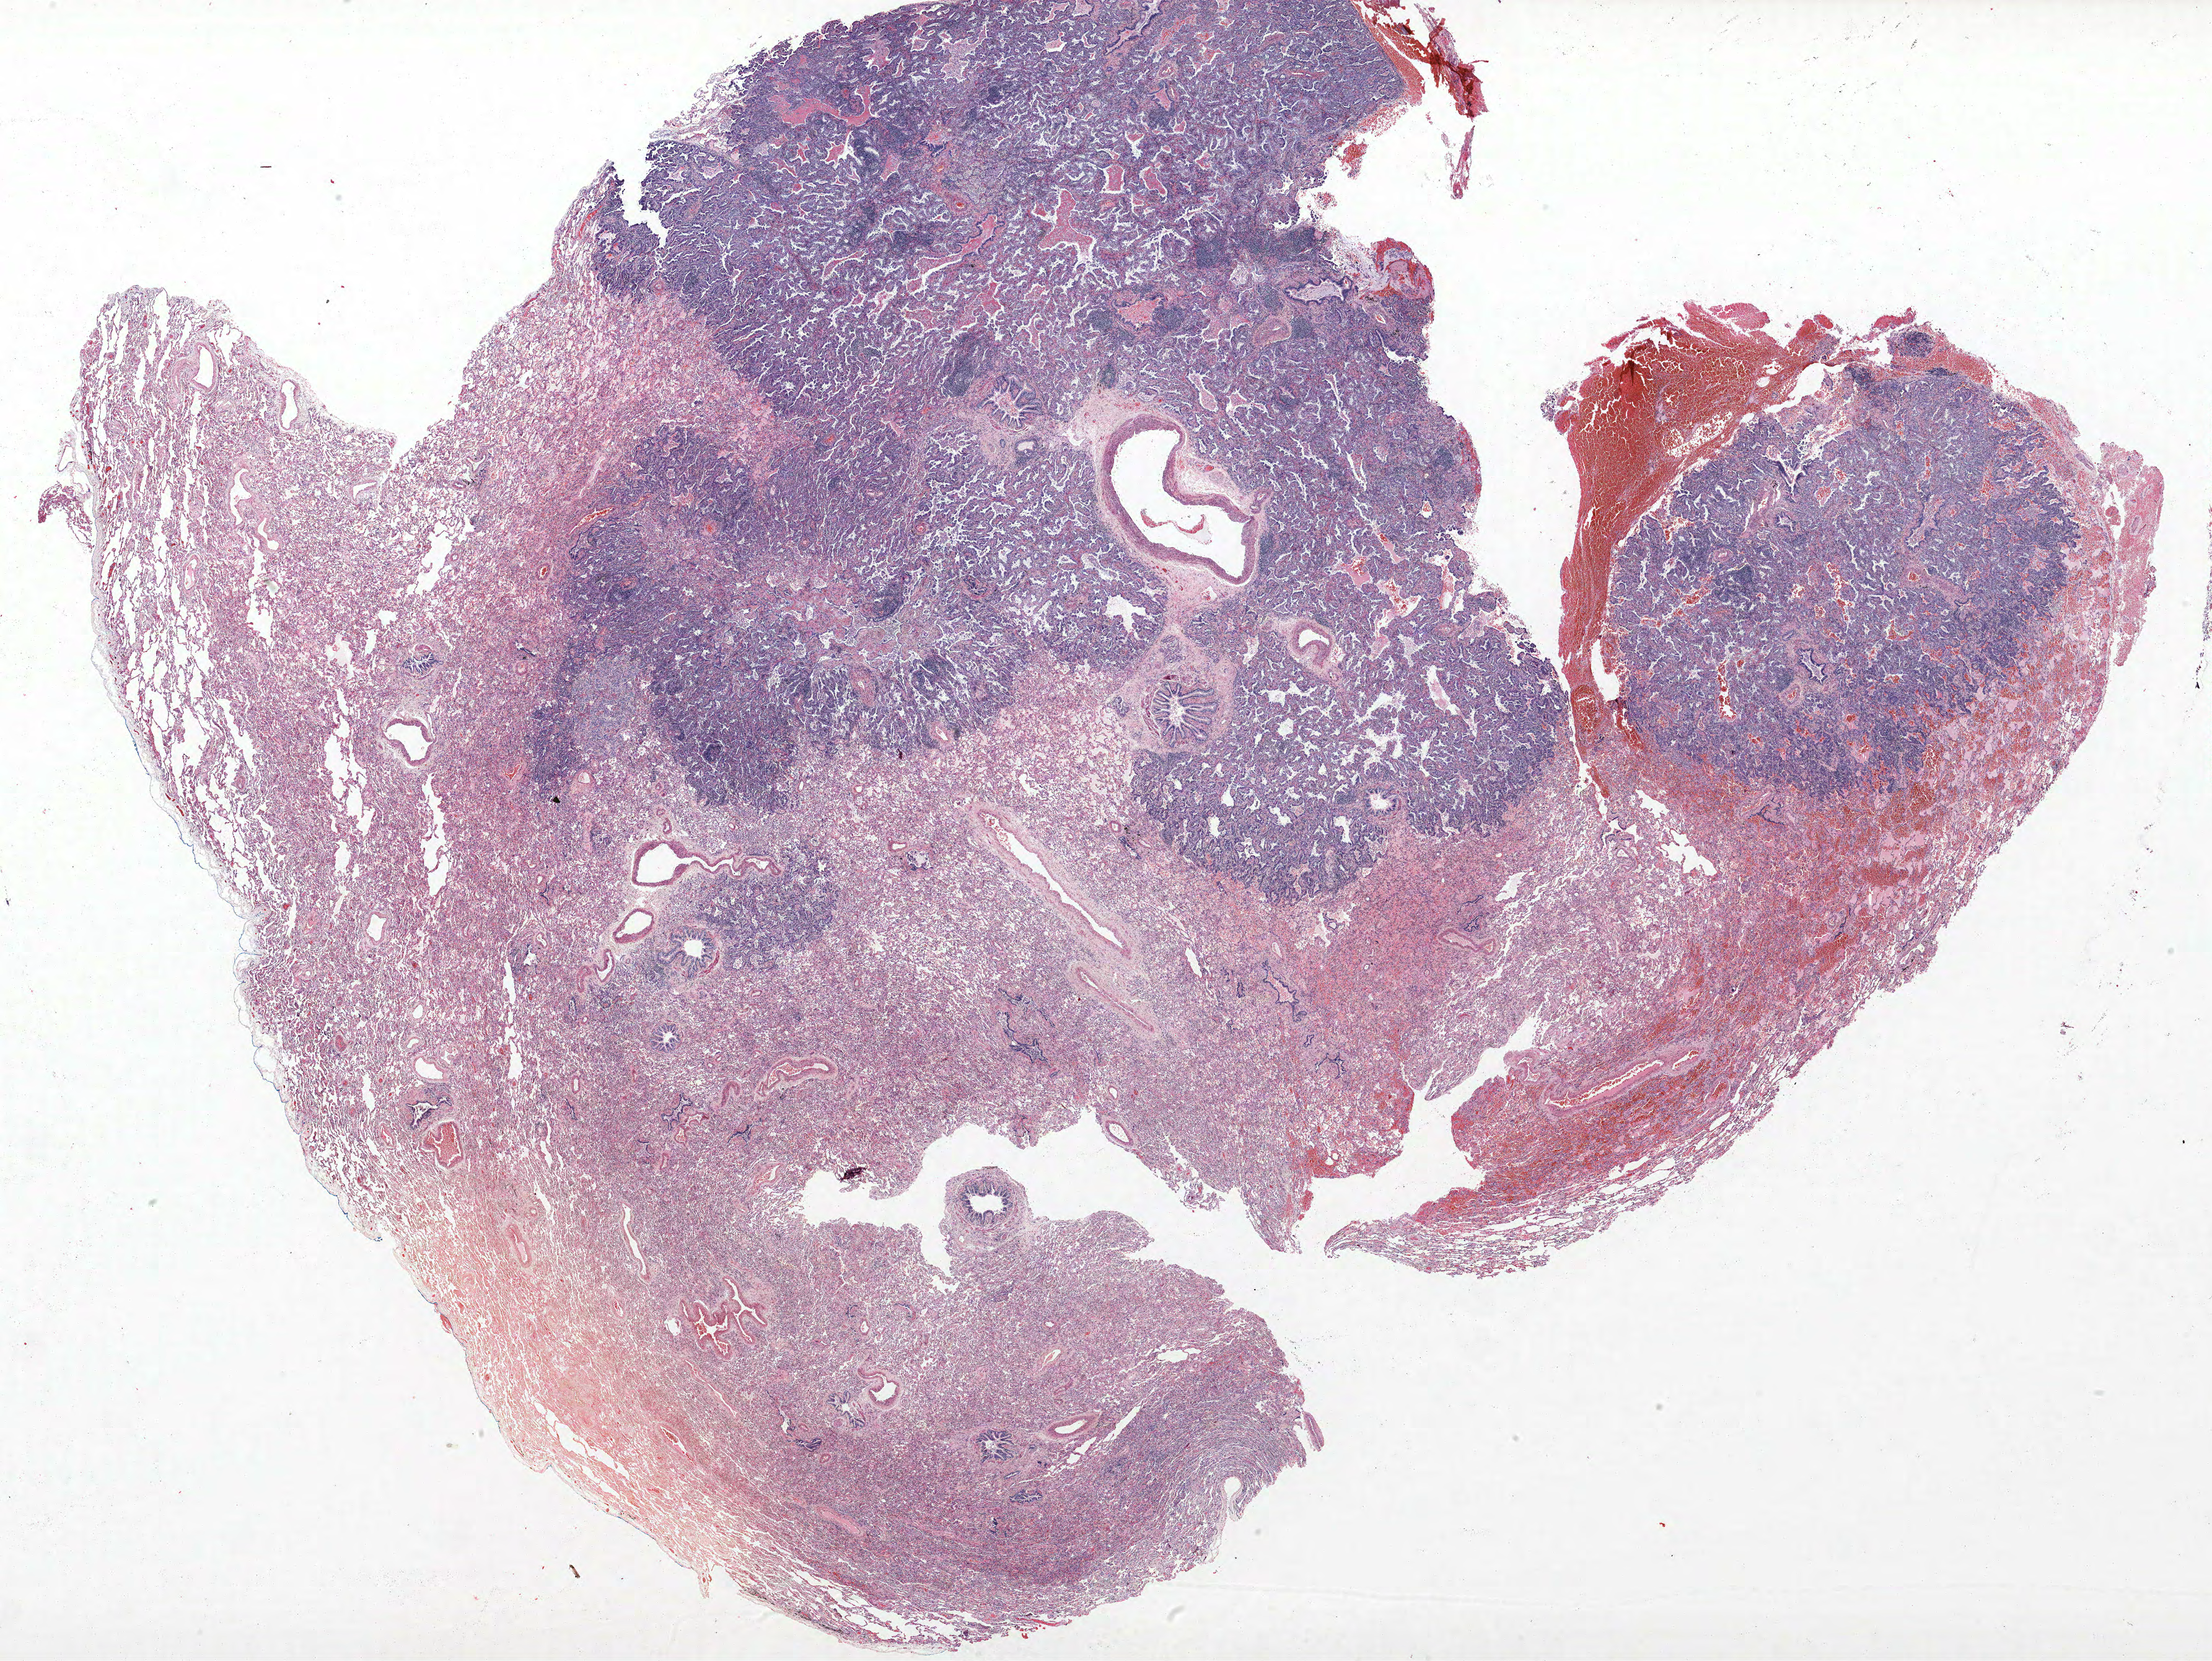
H&E whole-slide image, low-resolution overview of the scanned area, about 28.6 x 21.4 mm (from a 40x scan); formalin-fixed paraffin-embedded (FFPE) section; lung. Female, age 60 at enrolment. Former smoker at enrolment.
• primary tumour location (clinical record): right lower lobe
• participant's lung-cancer diagnosis: Bronchiolo-alveolar carcinoma, non-mucinous
• stage (AJCC 6th edition): IA
• tumour size (pathology): 15 mm